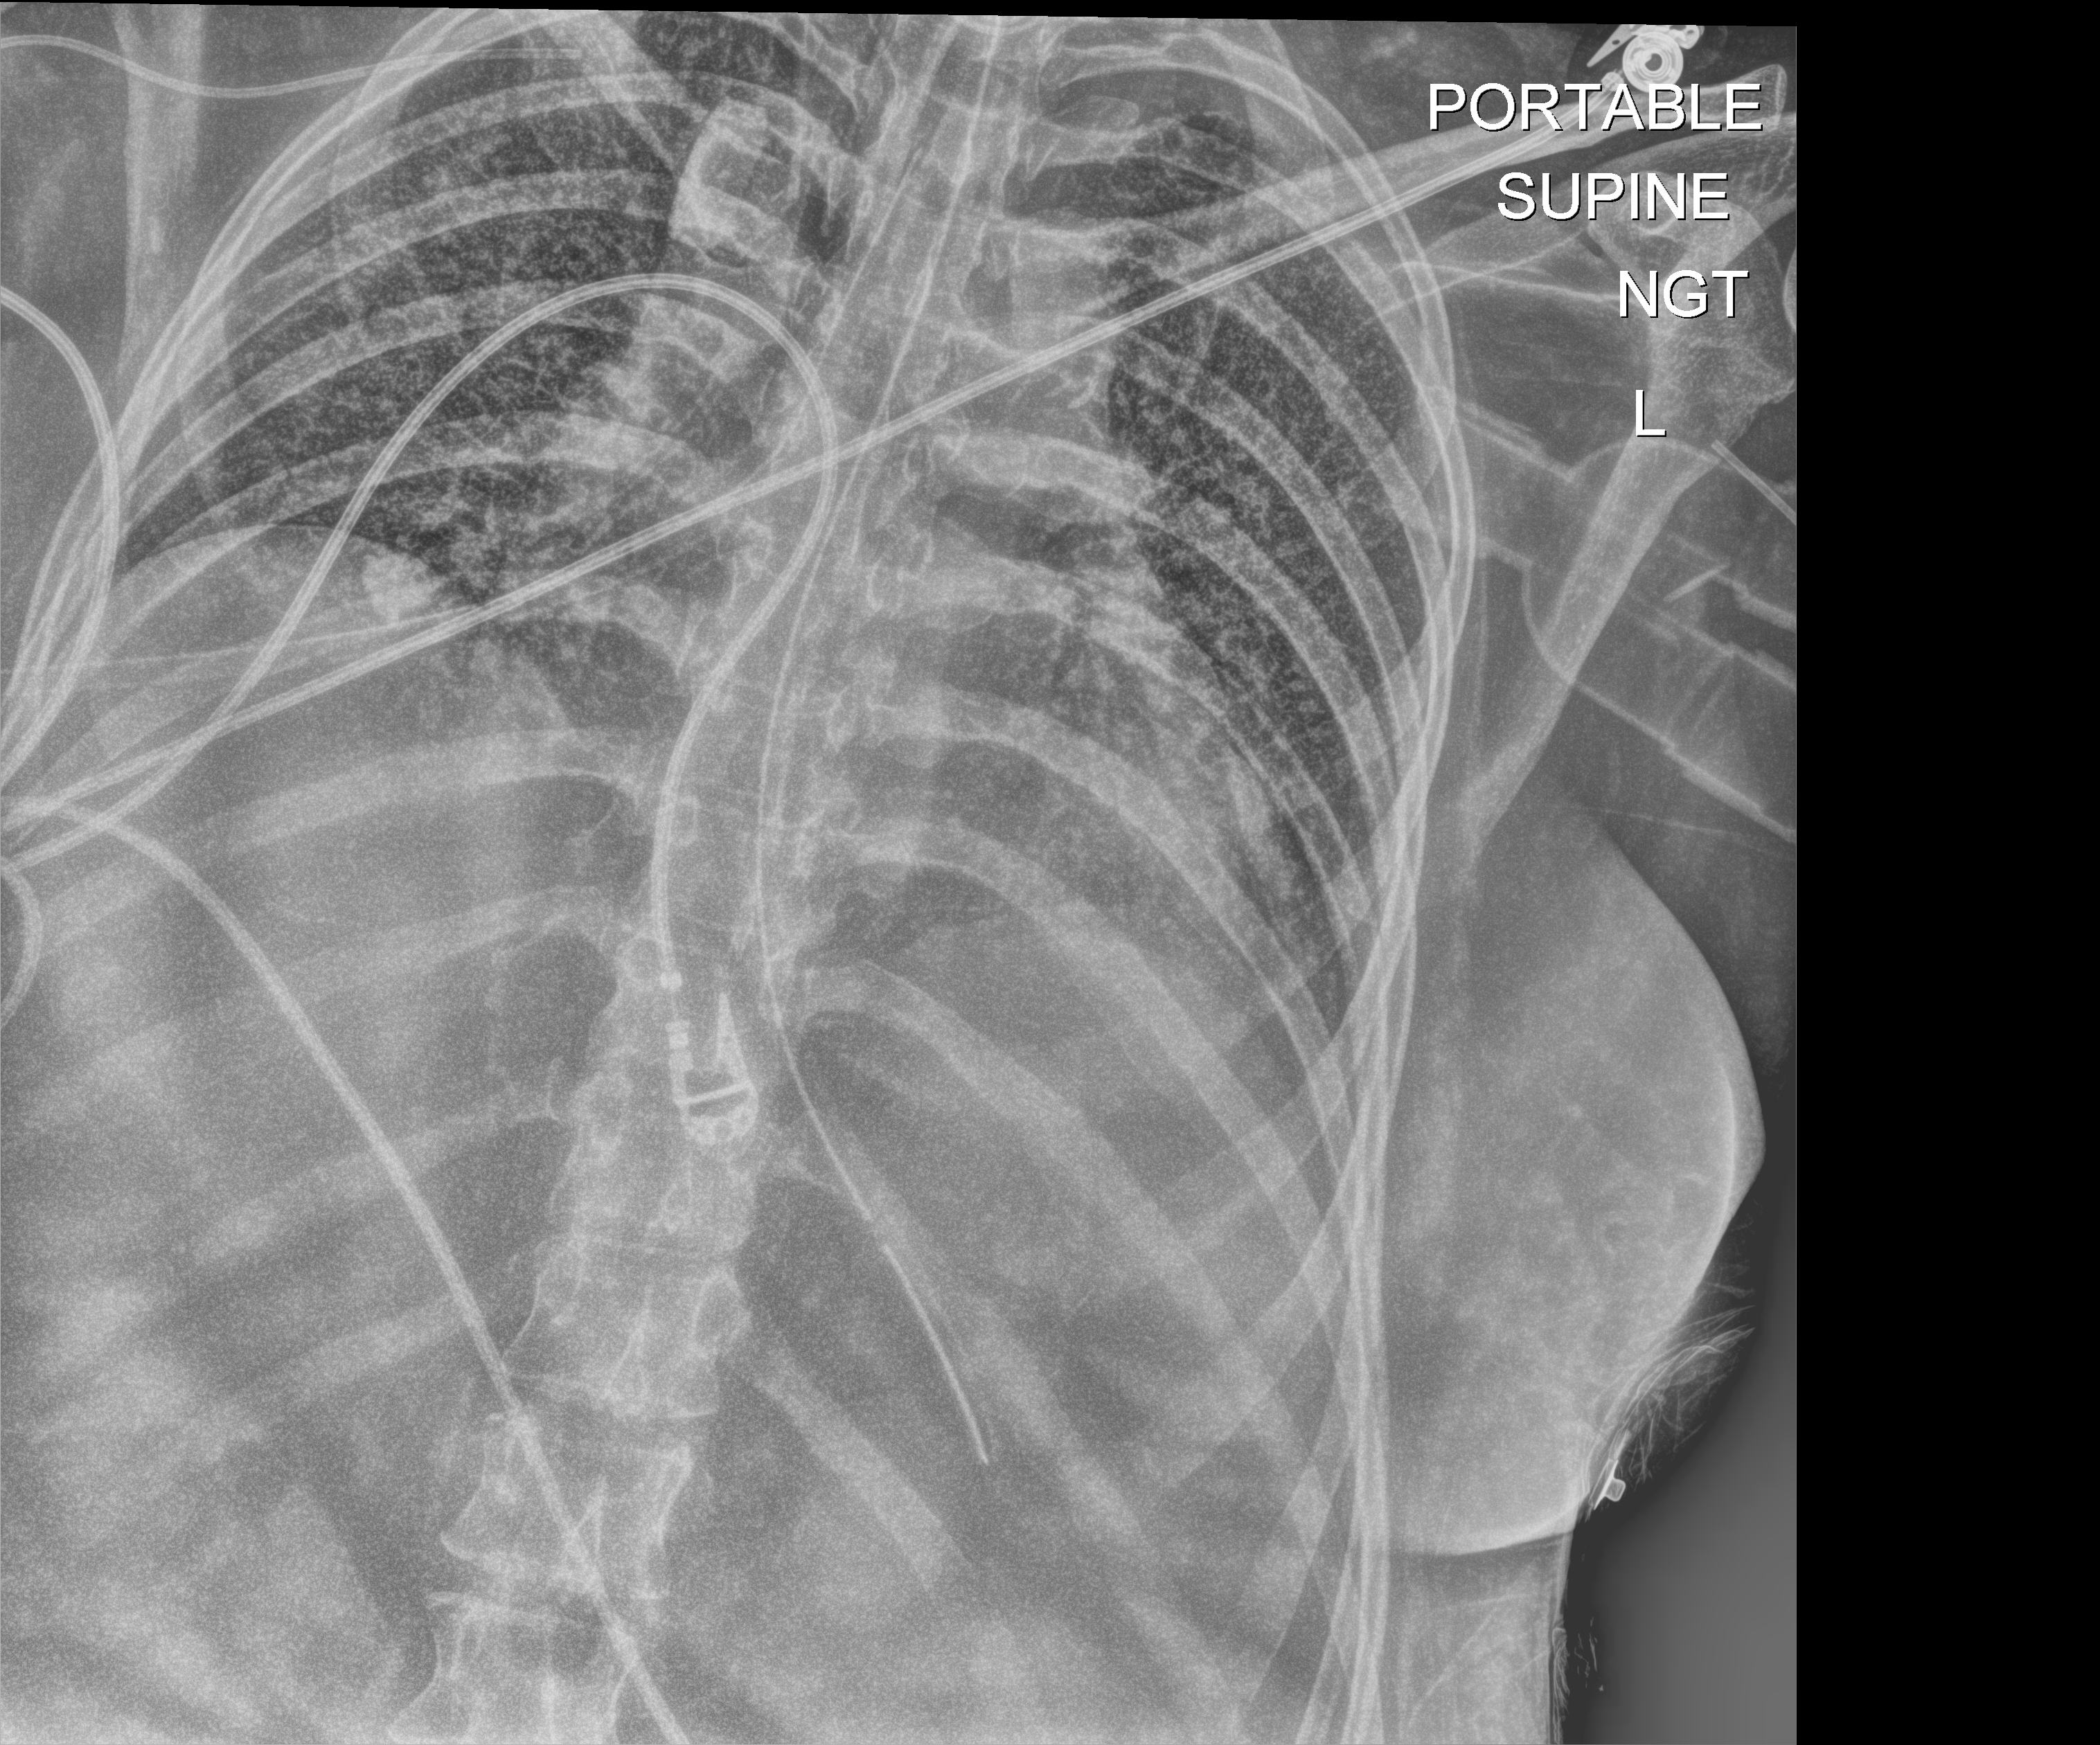
Bedside chest radiograph (digital radiography). Female patient hospitalised with COVID-19, age 18–59 years.
Hospital-stay facts (about this admission, not read from this image; timing relative to this image not recorded): smoking status (admission record): former; diabetes (admission record): no.